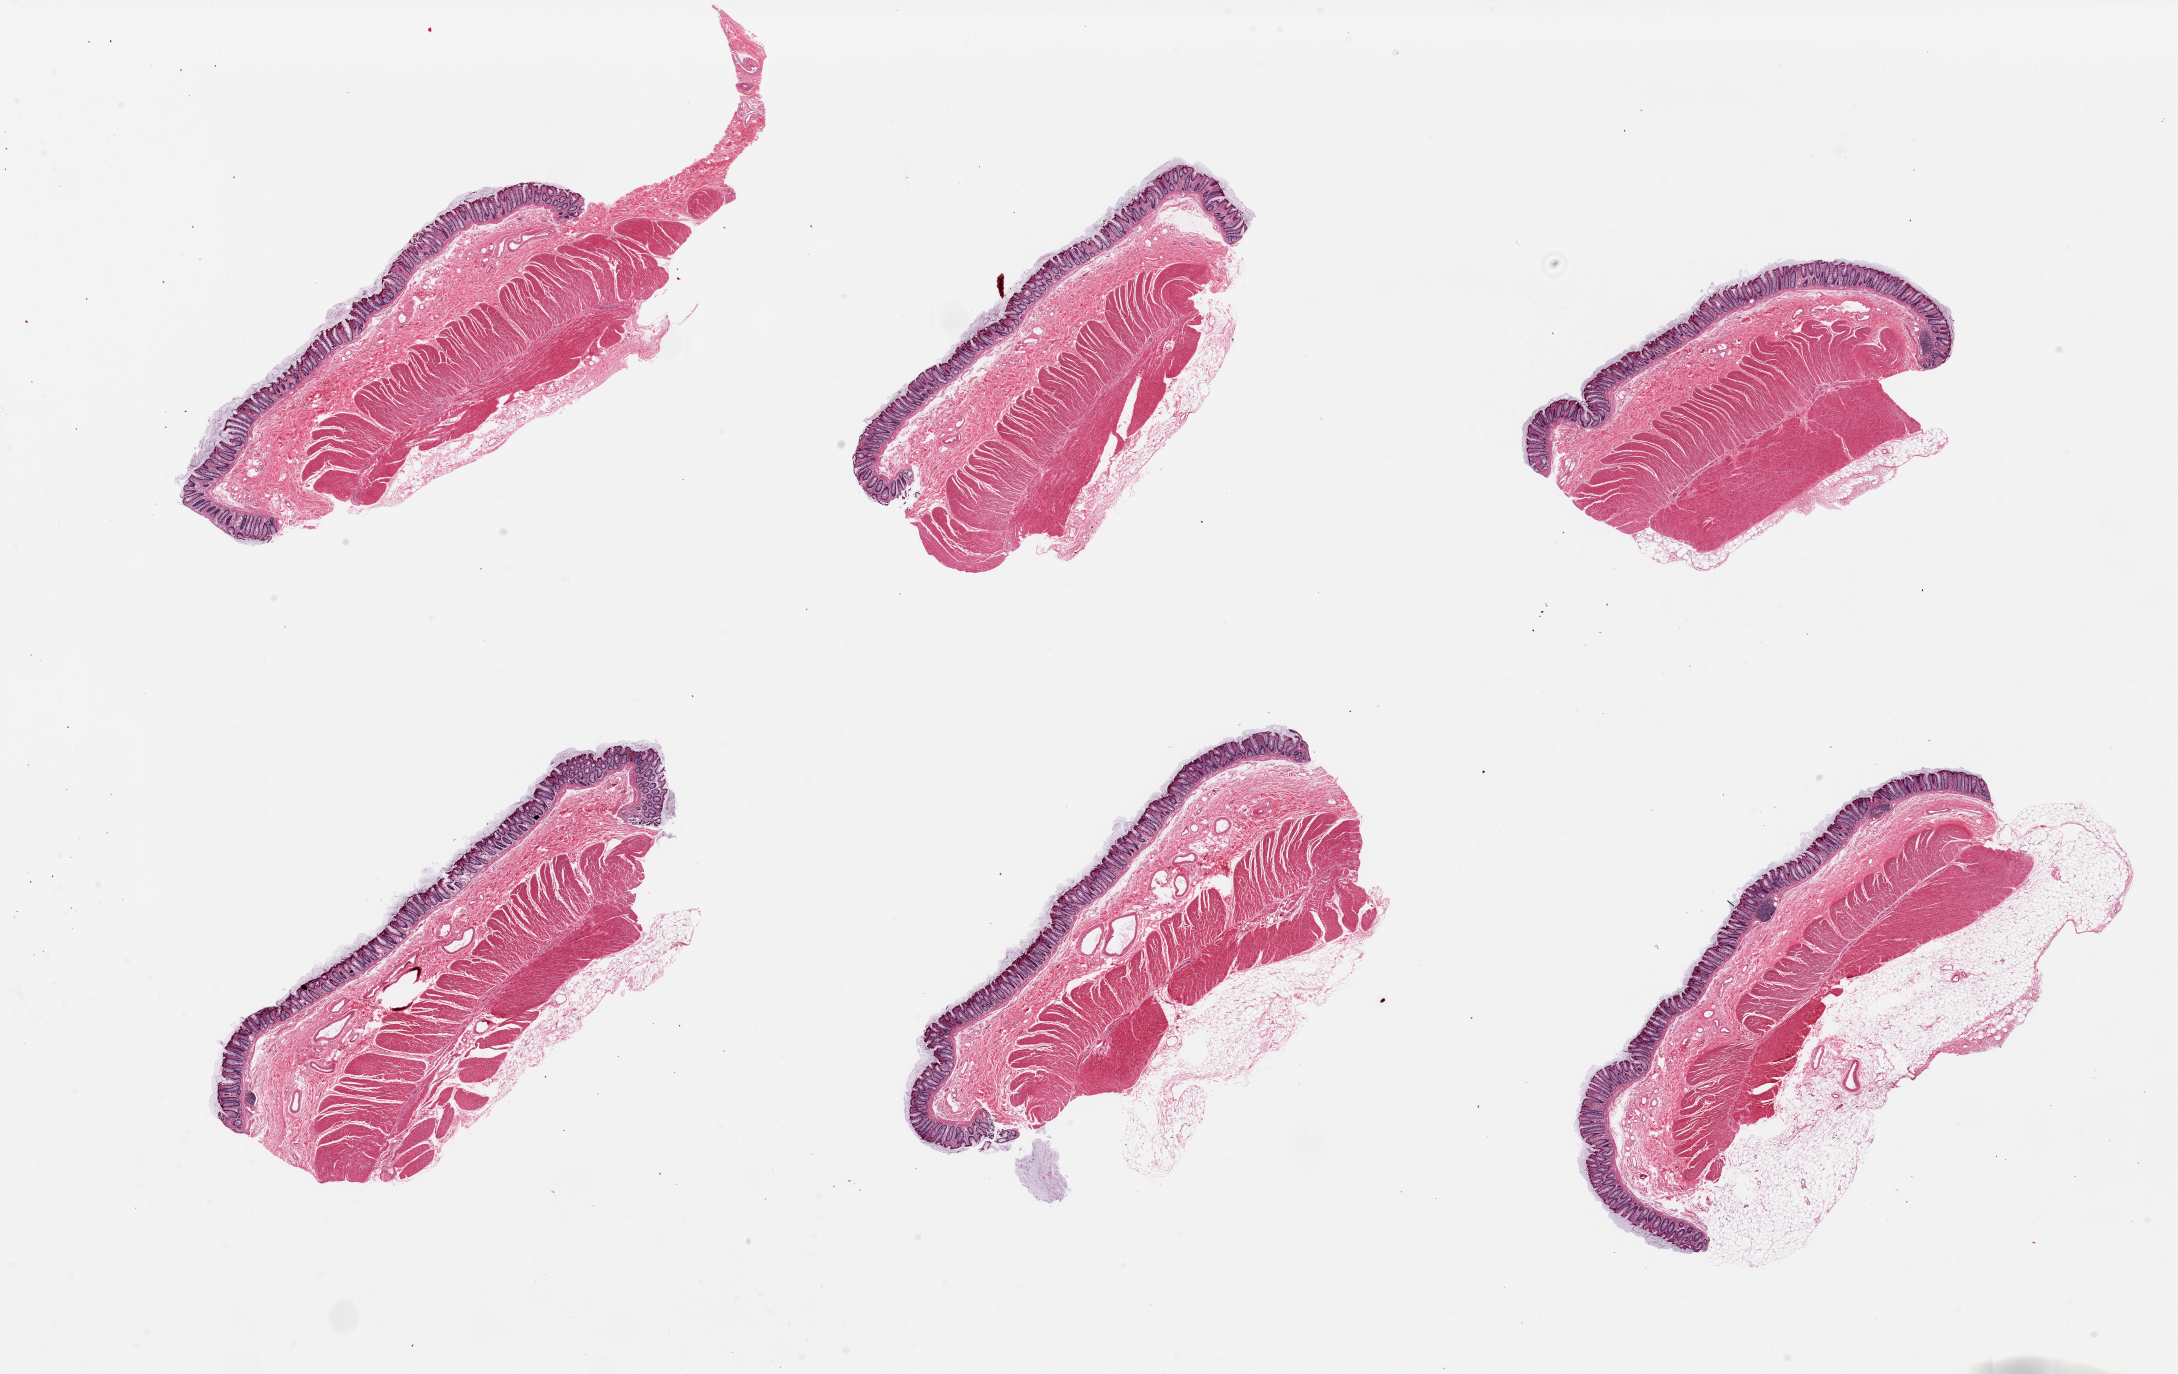
Digitized H&E-stained section, a low-resolution overview of the entire scanned area, about 34.5 x 21.7 mm (slide scanned at 20x), PAXgene-fixed paraffin-embedded (PFPE) section, section of transverse colon (target tissue), tissue donor sample. Male donor.
• pathologist's review note for this sample: 6 pieces; well preserved mucosa and full thickness wall in all; up to 2 mm pericolonic fat